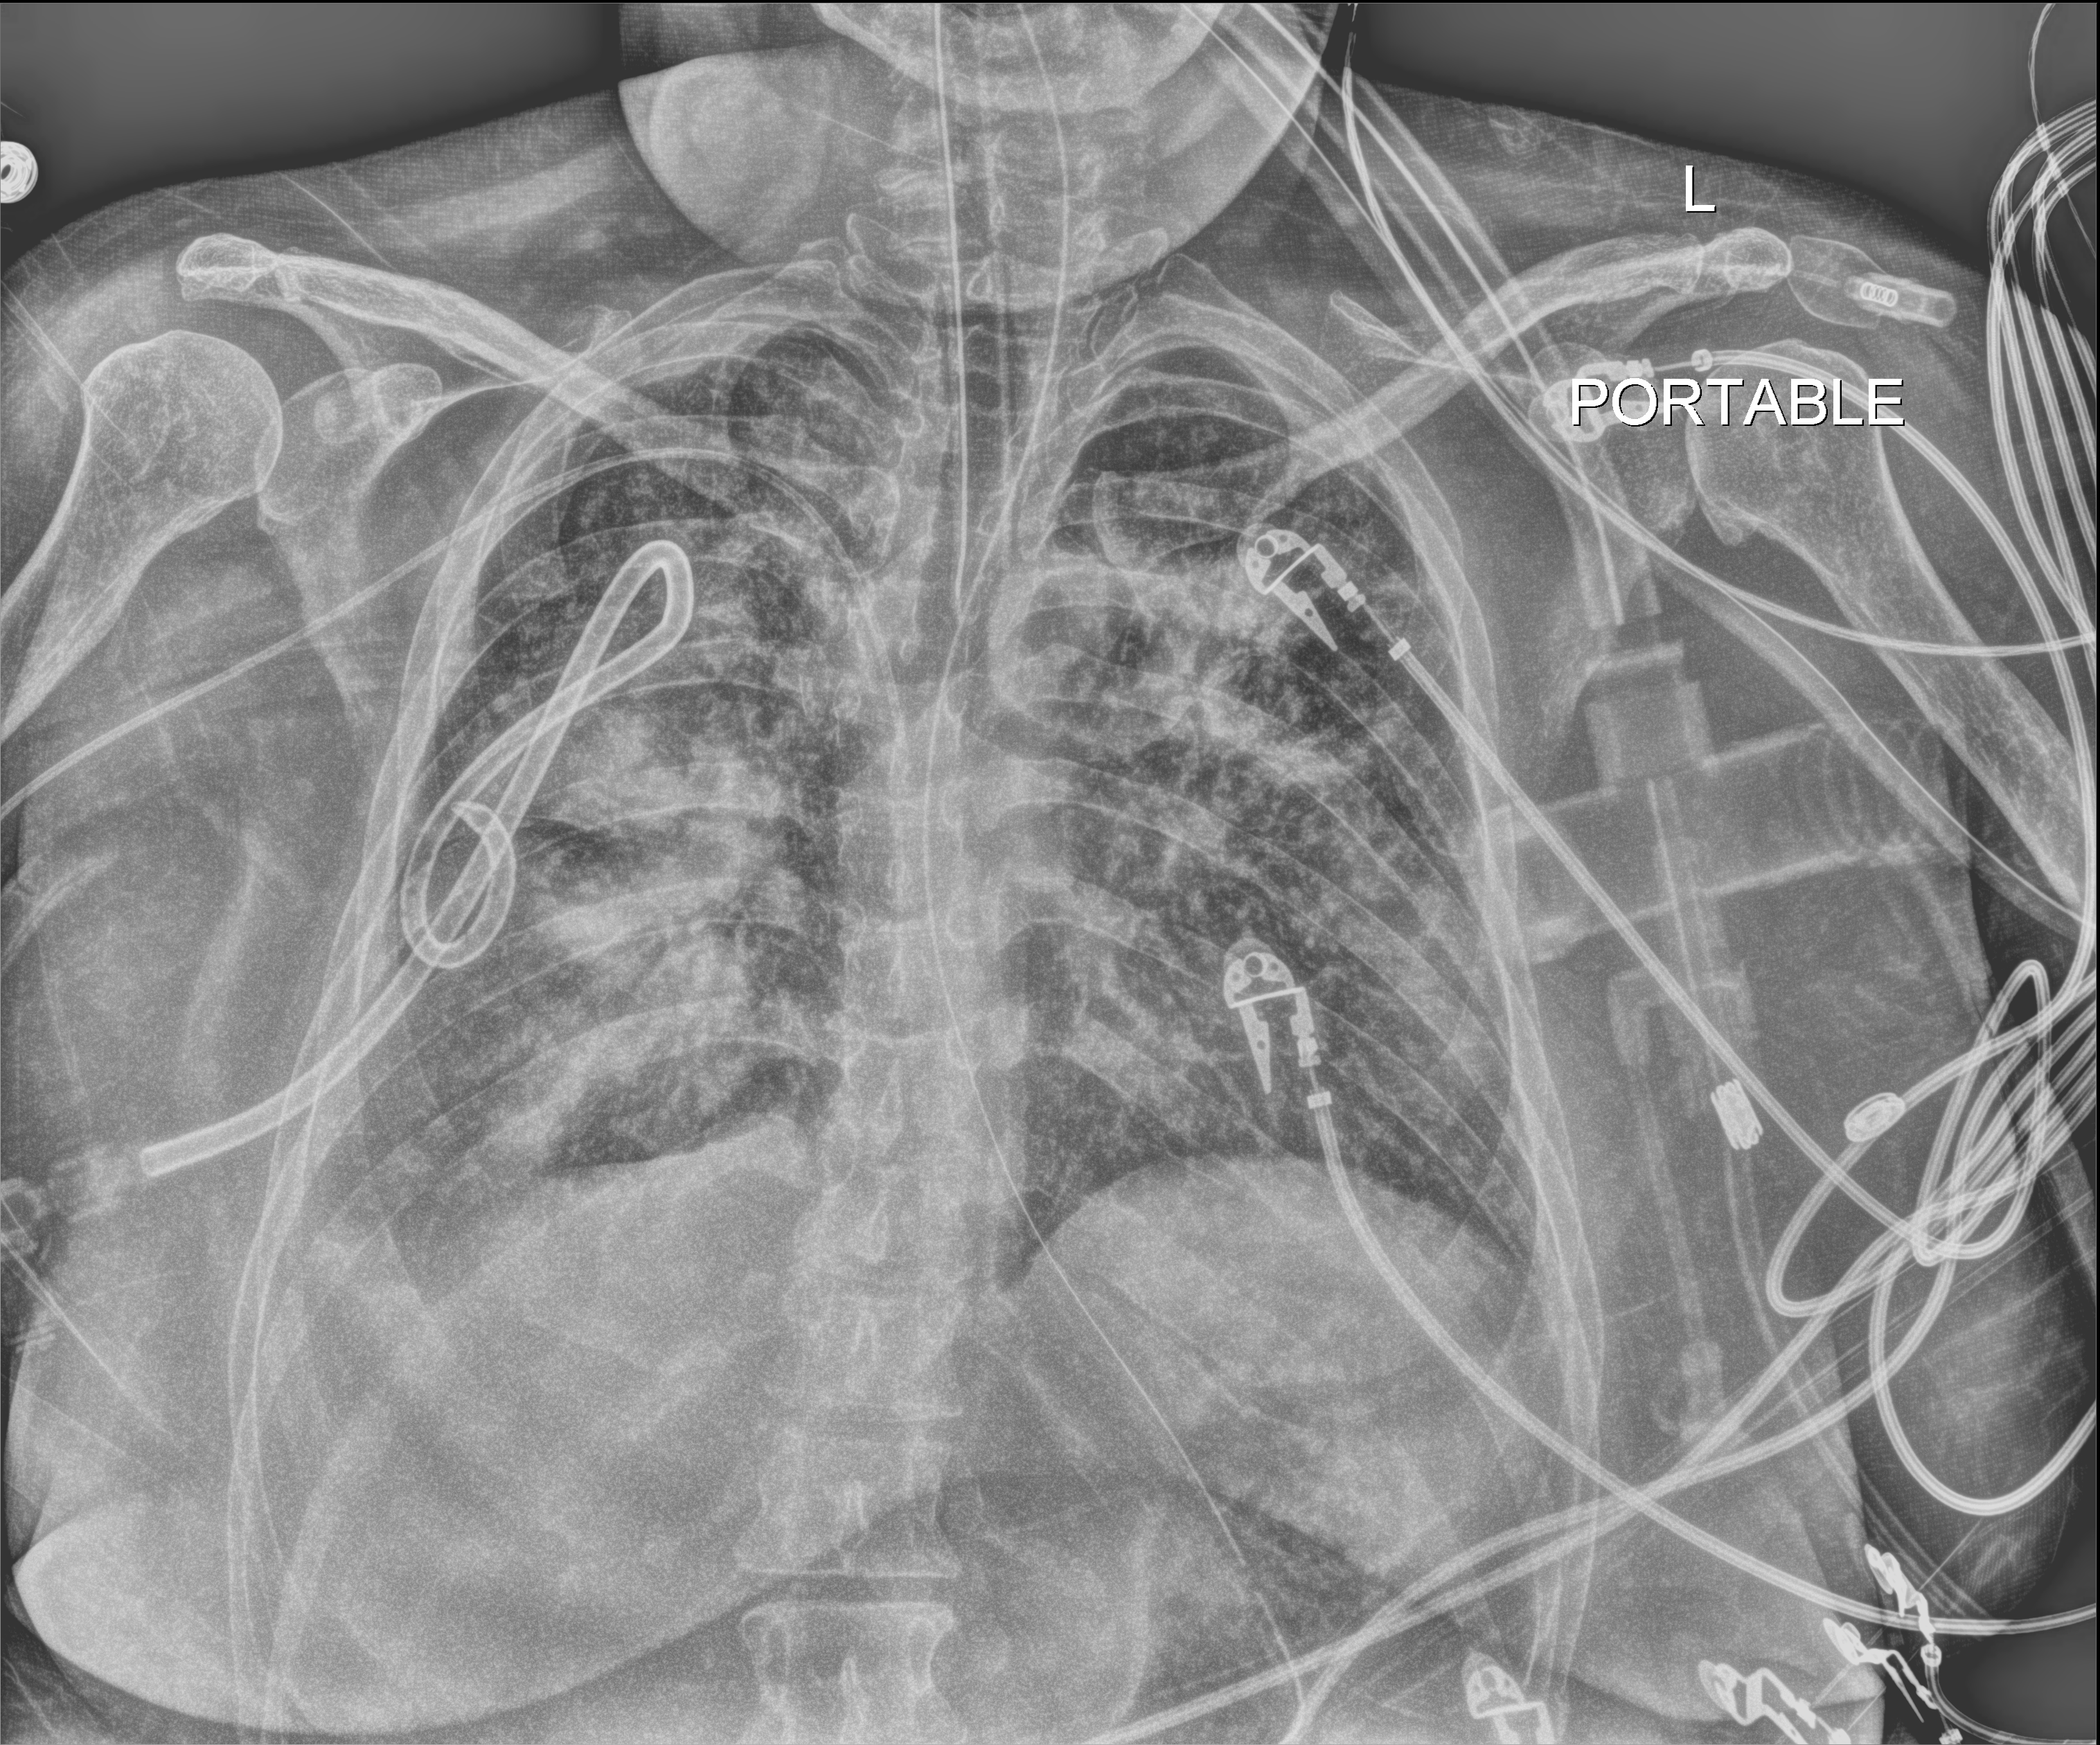
Chest X-ray (portable); anteroposterior (AP) projection. Adult patient hospitalised with COVID-19, age 18–59 years.
Hospital-stay facts (about this admission, not read from this image; timing relative to this image not recorded): admitted to intensive care during this hospital stay: yes.